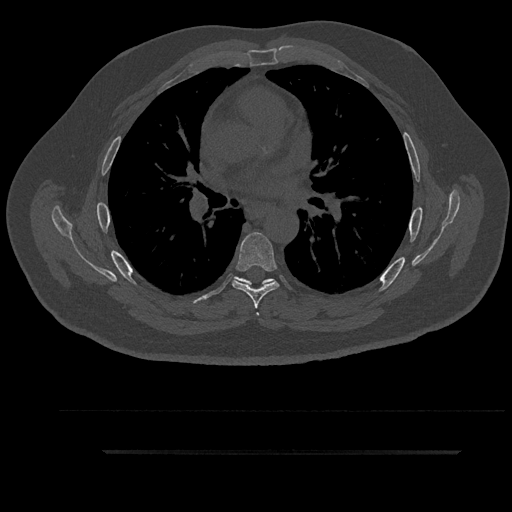
CT including the spine, one axial slice; slice 571 of 797 in the series (ordered by position); 120 kVp; bone window (W 1800 / L 400 HU); 0.5 mm slice thickness; 512 × 512 image matrix, field of view 432 × 432 mm. Male patient, age 63 years. Case-level facts recorded for this patient, not image findings: primary cancer: renal.
Annotated regions visible in this slice (semi-automatically segmented with operator editing):
- T5 vertebra: box from (x=235, y=277) to (x=274, y=316) px
- T6 vertebra: (x=232, y=232)–(x=279, y=309)
- T7 vertebra: (x=241, y=278)–(x=275, y=286)